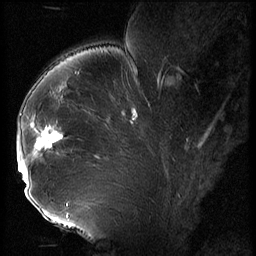
Breast MRI (dynamic contrast-enhanced), one sagittal slice; slice 38 of 56 in the series (ordered by position); 3 images stored at this slice position (order not interpretable as contrast timing); 1.5 T; TE 4.2 ms, TR 9 ms; 2.5 mm slice thickness; 256 × 256 image matrix, field of view 180 × 180 mm. Female patient, age 43 years. From the clinical record (not read from this slice): setting: breast cancer imaged before/during neoadjuvant chemotherapy; receptor status: HER2-positive.
Outlined on this slice (semi-automatic segmentation, software-assisted and operator-edited):
- analysis volume of interest (the breast-tissue region the enhancement analysis was run in; not a lesion): box from (x=18, y=92) to (x=74, y=211) px
- tumour enhancement mask (voxels above the 140 % enhancement threshold inside the analysis volume of interest): (x=18, y=126)–(x=64, y=185)